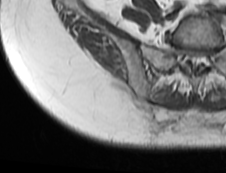
MRI of an extremity soft-tissue mass, one axial slice. Slice 58 of 73 in the series (ordered by position). MR volume resampled by the dataset authors to the PET/CT grid (not the native acquisition matrix). 3.27 mm slice thickness. 226 × 173 image matrix. Female patient. Case-level facts recorded for this patient, not image findings: histological type: spindle cell suggestive of myxofibrosarcoma; grade: intermediate; site of the primary tumour: right buttock.
Structures marked on this image (expert contour drawn on MRI and transferred to this co-registered scan by the dataset authors):
- gross tumour volume (mass): box from (x=125, y=94) to (x=179, y=125) px